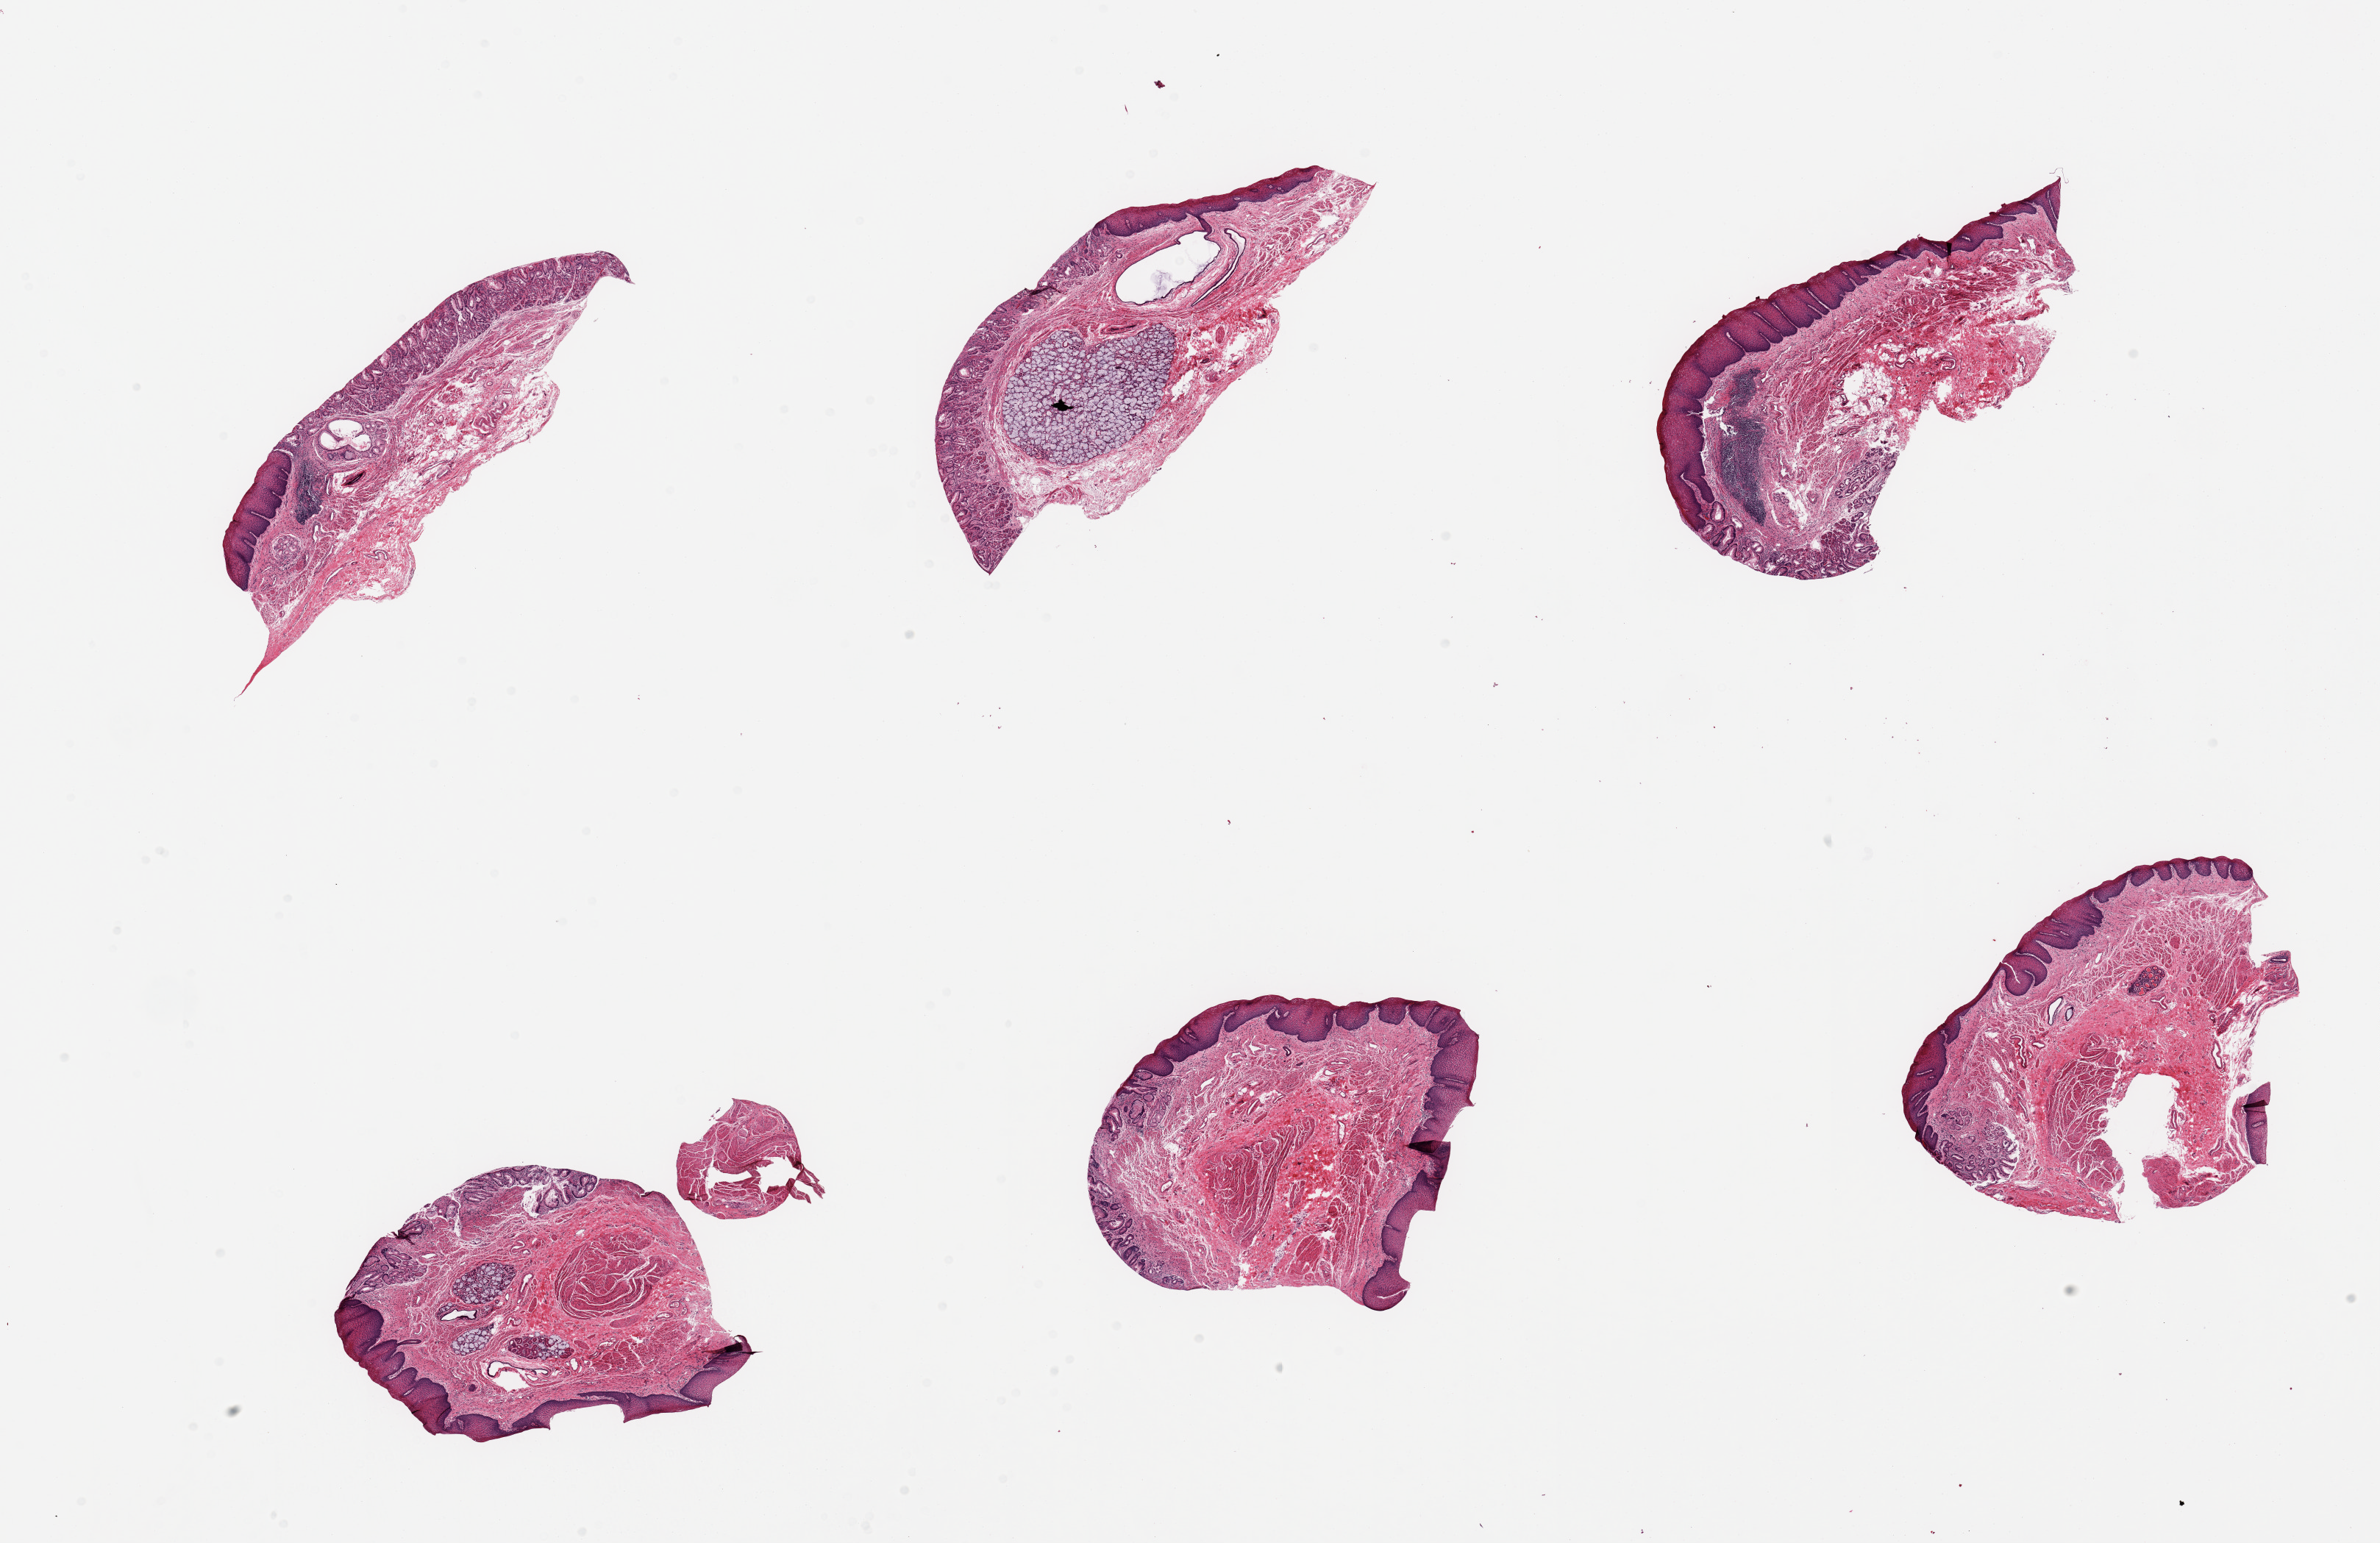
Digitized haematoxylin and eosin-stained section, brightfield — shown as a low-resolution overview of the whole scanned area (about 25.6 x 16.6 mm, acquisition: 20x scan), PAXgene-fixed paraffin-embedded (PFPE) section, section of gastroesophageal junction (target tissue), tissue donor sample.
• review note (as recorded): 6 pieces; all have mucosa, no muscularis propria